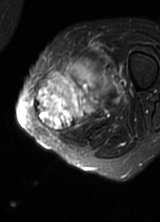
MRI of an extremity soft-tissue mass, one axial slice. Position 20 of 69 along the scan axis. T2-weighted fat-saturated. MR volume resampled by the dataset authors to the PET/CT grid (not the native acquisition matrix). 3.27 mm slice thickness. 160 × 222 image matrix. Female patient. From the clinical record (not read from this slice): histological type: pleomorphic leiomyosarcoma; grade: high; site of the primary tumour: left thigh.
Structures marked on this image (expert contour drawn on MRI and transferred to this co-registered scan by the dataset authors):
- gross tumour volume including surrounding oedema: bounding box <34,56,119,133> (left, top, right, bottom; pixels)
- gross tumour volume (mass): <34,77,99,131>